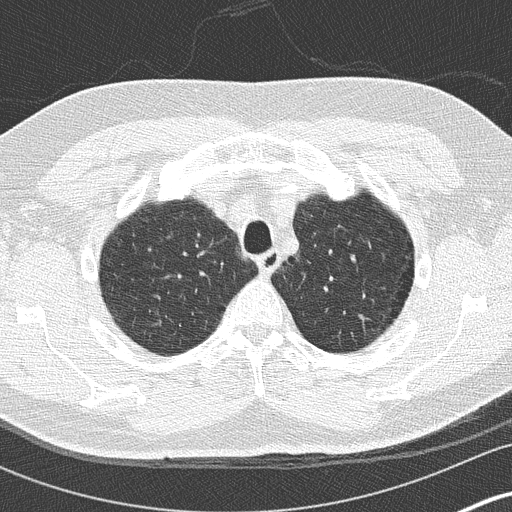
Chest CT (low-dose screening protocol), one axial image; baseline screening round; lung window (W 1500 / L -600 HU); 2 mm slice thickness; lung (sharp) reconstruction kernel (B50f). Male participant, aged 59 years at enrolment. Current smoker at enrolment.
Expert-annotated lung lesion, bounding box <139,294,189,343> (left, top, right, bottom; pixels). The exam's reader record, not a measurement of the box and not confirmed to be the same lesion: non-calcified nodule or mass ≥4 mm, right upper lobe, 16 × 16 mm, ground glass attenuation. Later outcome: lung cancer diagnosed 456 days after this screen — bronchiolo-alveolar adenocarcinoma, NOS, right lower lobe, stage IA (AJCC 6th edition), 15 mm at pathology.